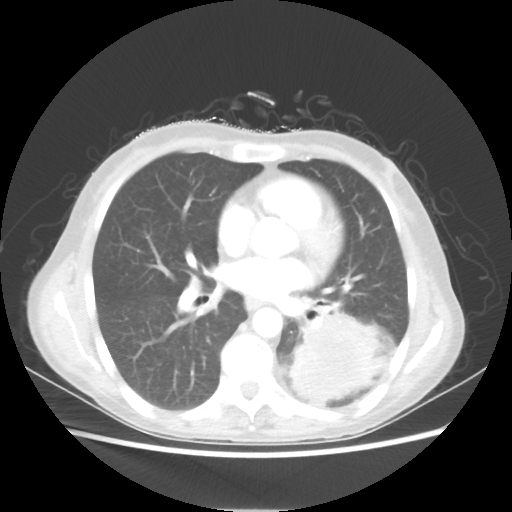
Chest CT, one axial slice; slice 27 of 56 in the series (ordered by position); reconstruction kernel STANDARD; 80 kVp; lung window (W 1500 / L -600 HU); 5 mm slice thickness; 512 × 512 image matrix, field of view 360 × 360 mm. Patient: female, 53 years. Case-level facts recorded for this patient, not image findings: clinical TNM (as recorded): T3 N0 M0.
Structures marked on this image (bounding box drawn by a radiologist):
- lung tumour (recorded histology: adenocarcinoma): bounding box (x1, y1, x2, y2) in pixels: (290, 314, 390, 410)